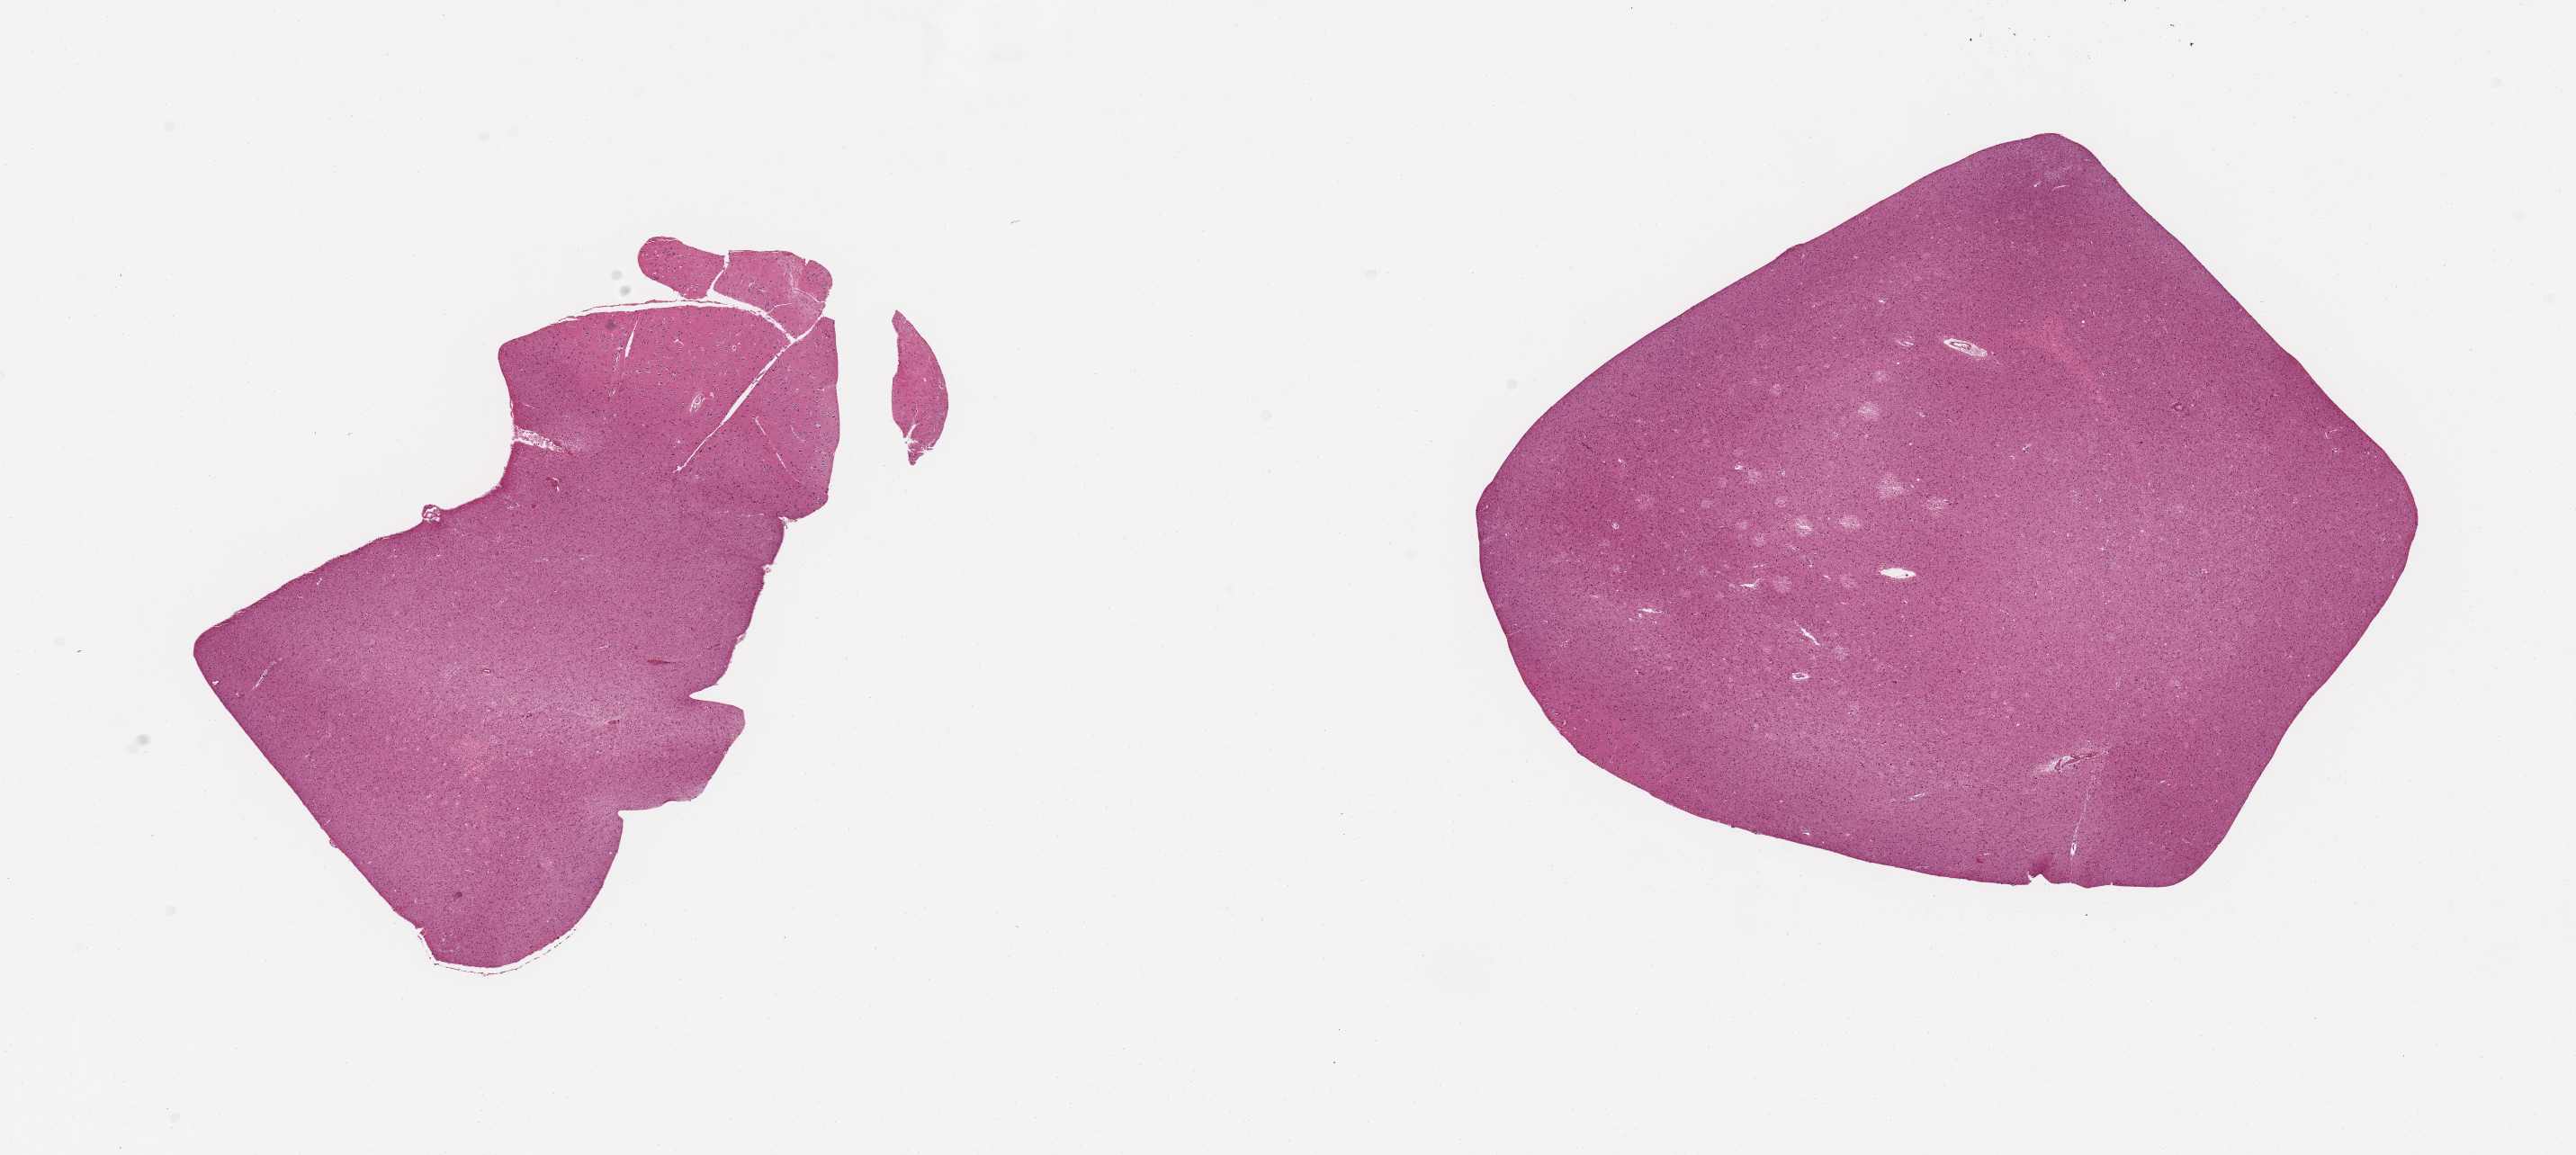
Haematoxylin and eosin whole-slide image, shown as a low-resolution overview of the whole scanned area (about 22.6 x 10.2 mm, from a 20x scan), PAXgene-fixed paraffin-embedded (PFPE) section, sampled site (target tissue): cerebral cortex, tissue donor sample. Donor: male.
* review note (as recorded): 2 pieces, no abnormalties